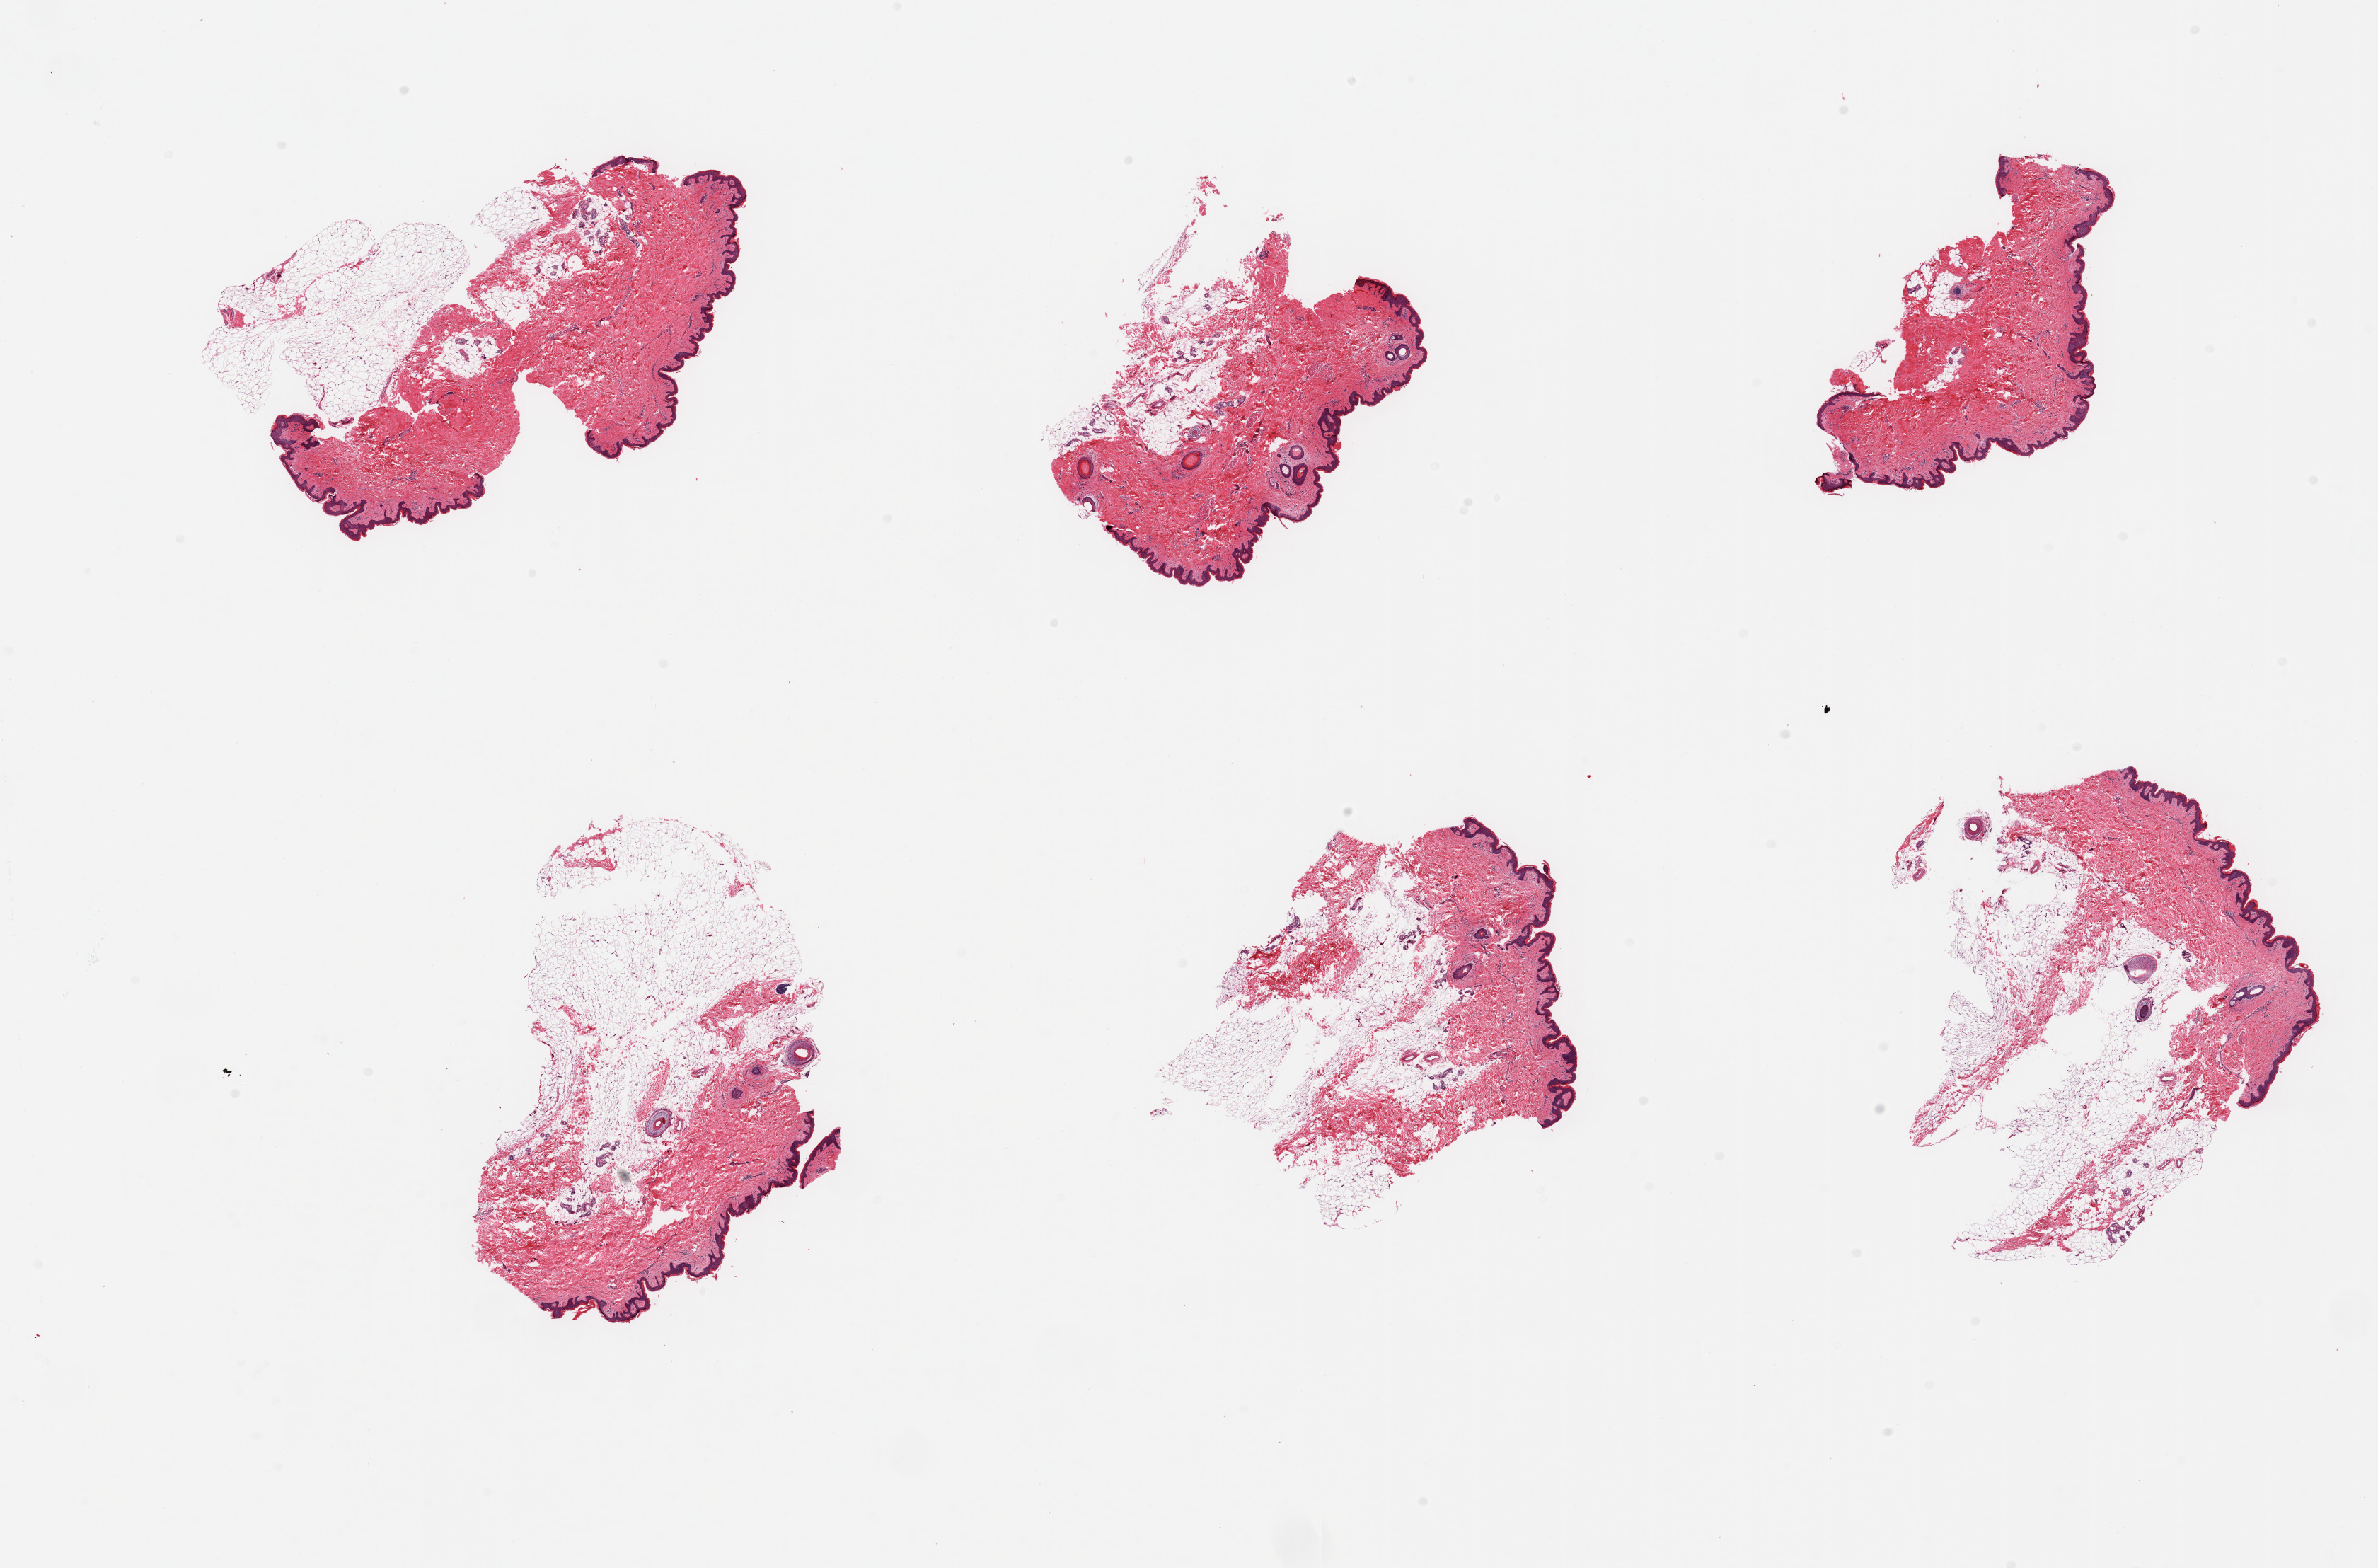
Digitized hematoxylin and eosin (H&E)-stained section, shown as a low-resolution overview of the whole scanned area (about 26.6 x 17.5 mm, acquisition: 20x scan). PAXgene-fixed paraffin-embedded (PFPE) section. Target tissue: skin of suprapubic region. Tissue donor sample. Donor sex: female.
* reviewer comment on this tissue sample: 6 pieces; 5 include significant attached fat, up to 70%